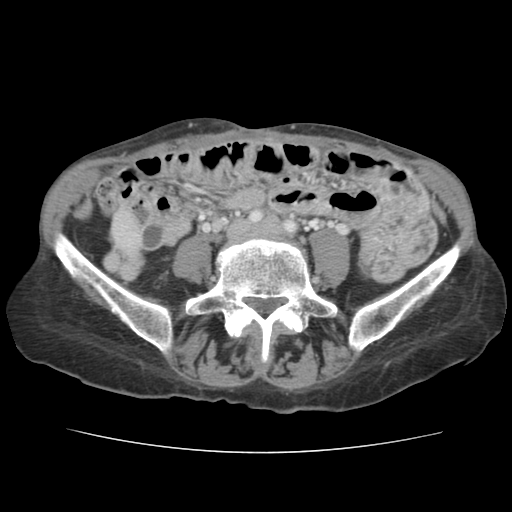
Contrast-enhanced abdominal CT, one axial slice. Slice 8 of 136 in the series (ordered by position). 120 kVp. Intravenous contrast given. Soft-tissue window (W 400 / L 40 HU). 2.5 mm slice thickness. 512 × 512 image matrix, field of view 319 × 319 mm. Female patient, age 77 years. From the clinical record (not read from this slice): diagnosis: colorectal cancer liver metastases, imaged before liver resection; multiple liver metastases: yes; largest metastasis: 3 cm; chemotherapy before resection: yes.
Outlined on this slice (expert manual segmentation):
- liver: box from (x=114, y=211) to (x=139, y=249) px